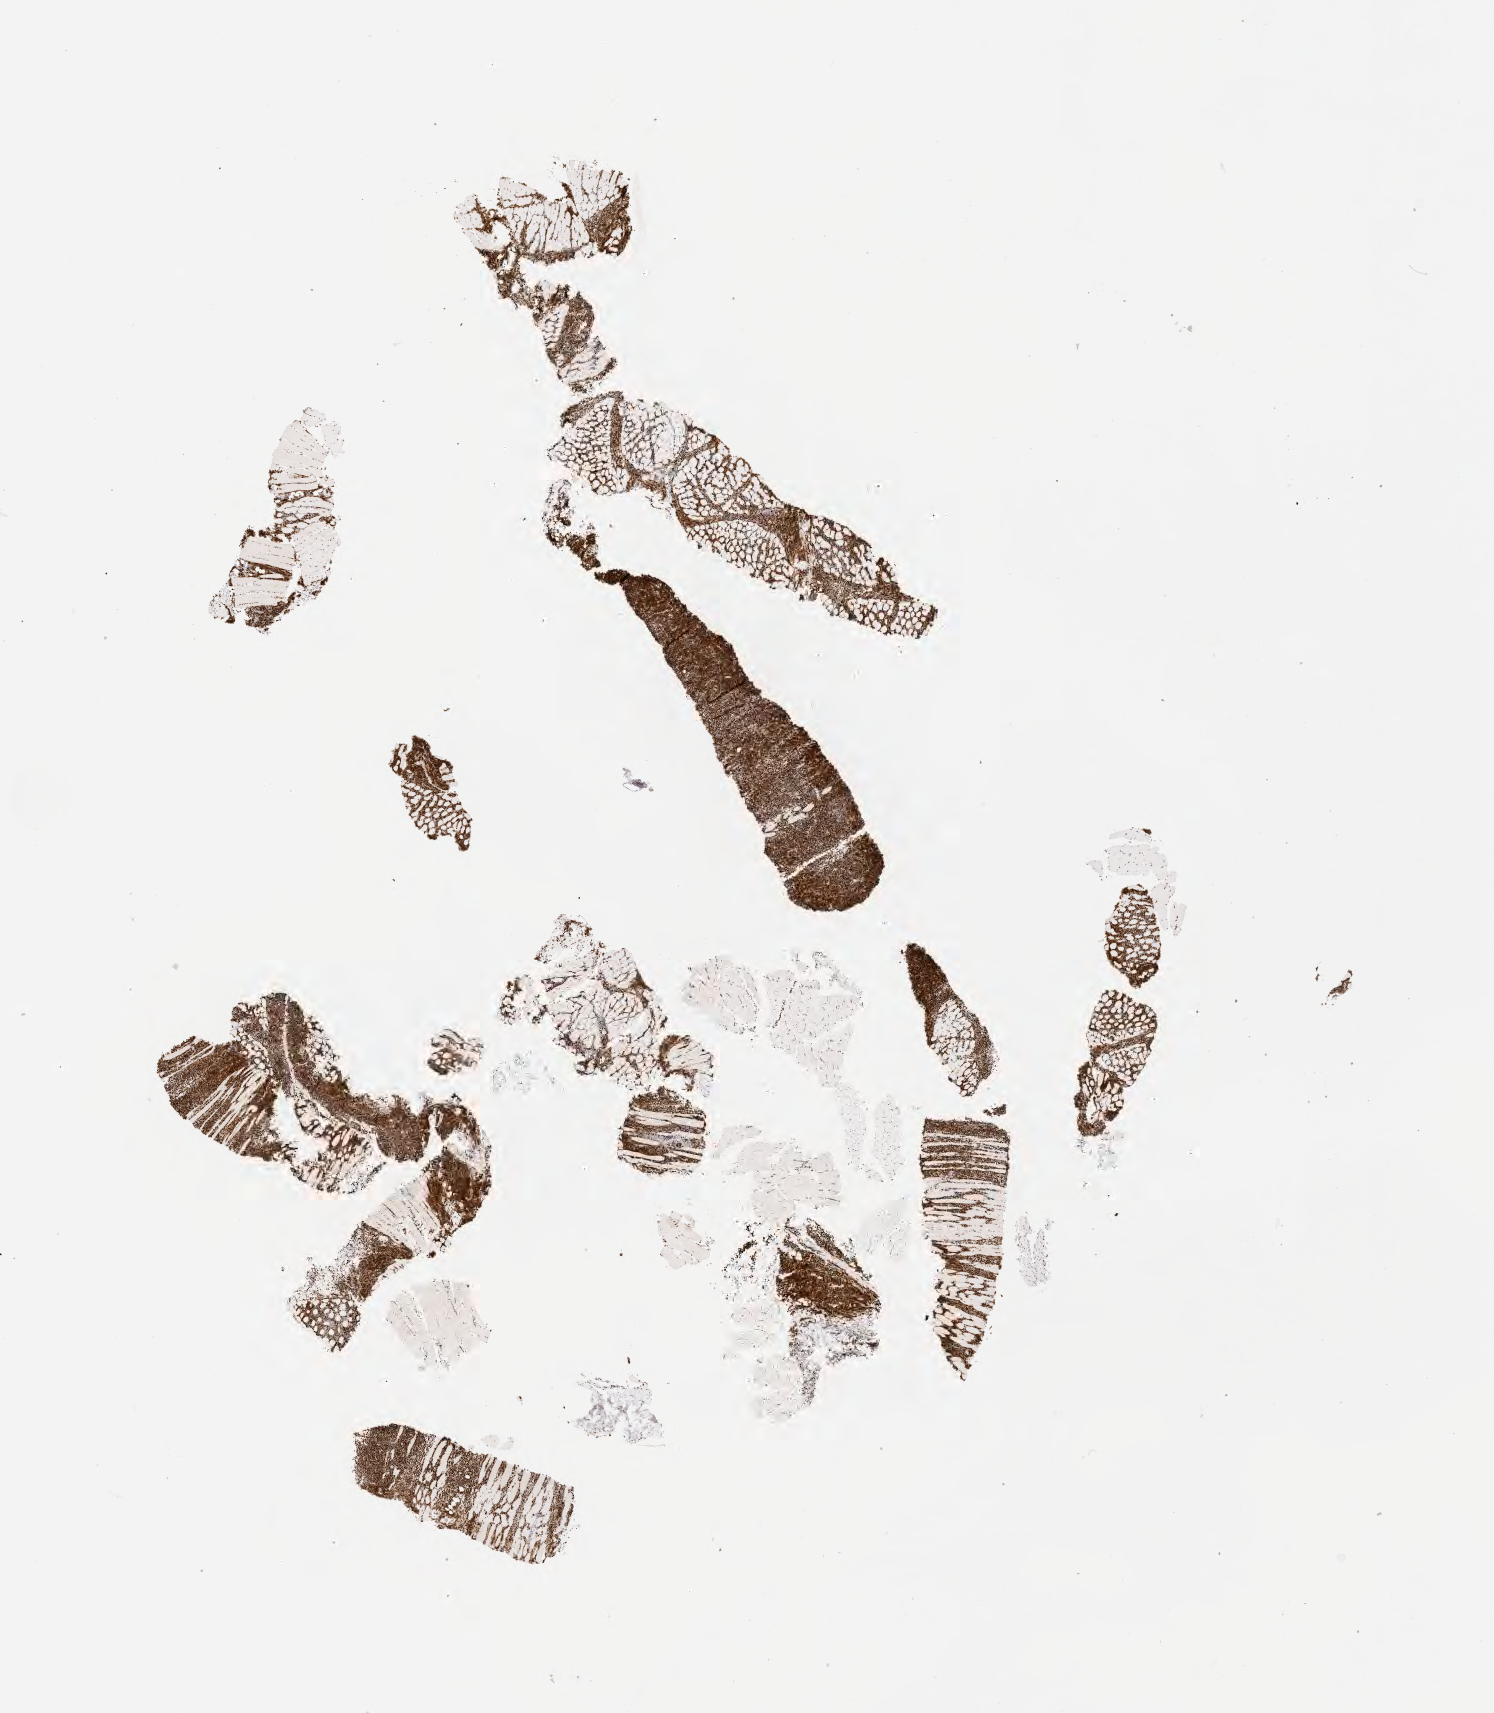
Whole-slide image, immunohistochemical stain for BCL6 — shown as a low-resolution overview of the whole scanned area (about 12.1 x 13.8 mm); tumor tissue; anatomic site: retroperitoneum. Female patient, aged 53.
Histologic diagnosis: Burkitt lymphoma, NOS.